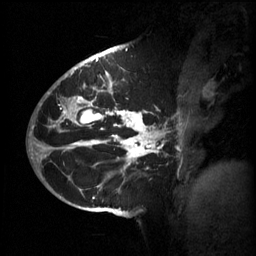
Breast MRI (dynamic contrast-enhanced), one sagittal slice. Slice 34 of 60 in the series (ordered by position). 3 images stored at this slice position (order not interpretable as contrast timing). 1.5 T. TE 4.2 ms, TR 11 ms. 2 mm slice thickness. 256 × 256 image matrix, field of view 220 × 220 mm. Female patient, age 51 years.
Structures marked on this image (semi-automatic segmentation, software-assisted and operator-edited):
- analysis volume of interest (the breast-tissue region the enhancement analysis was run in; not a lesion): bounding box (x1, y1, x2, y2) in pixels: (63, 80, 186, 201)
- tumour enhancement mask (voxels above the 70 % enhancement threshold inside the analysis volume of interest): (63, 80, 165, 199)